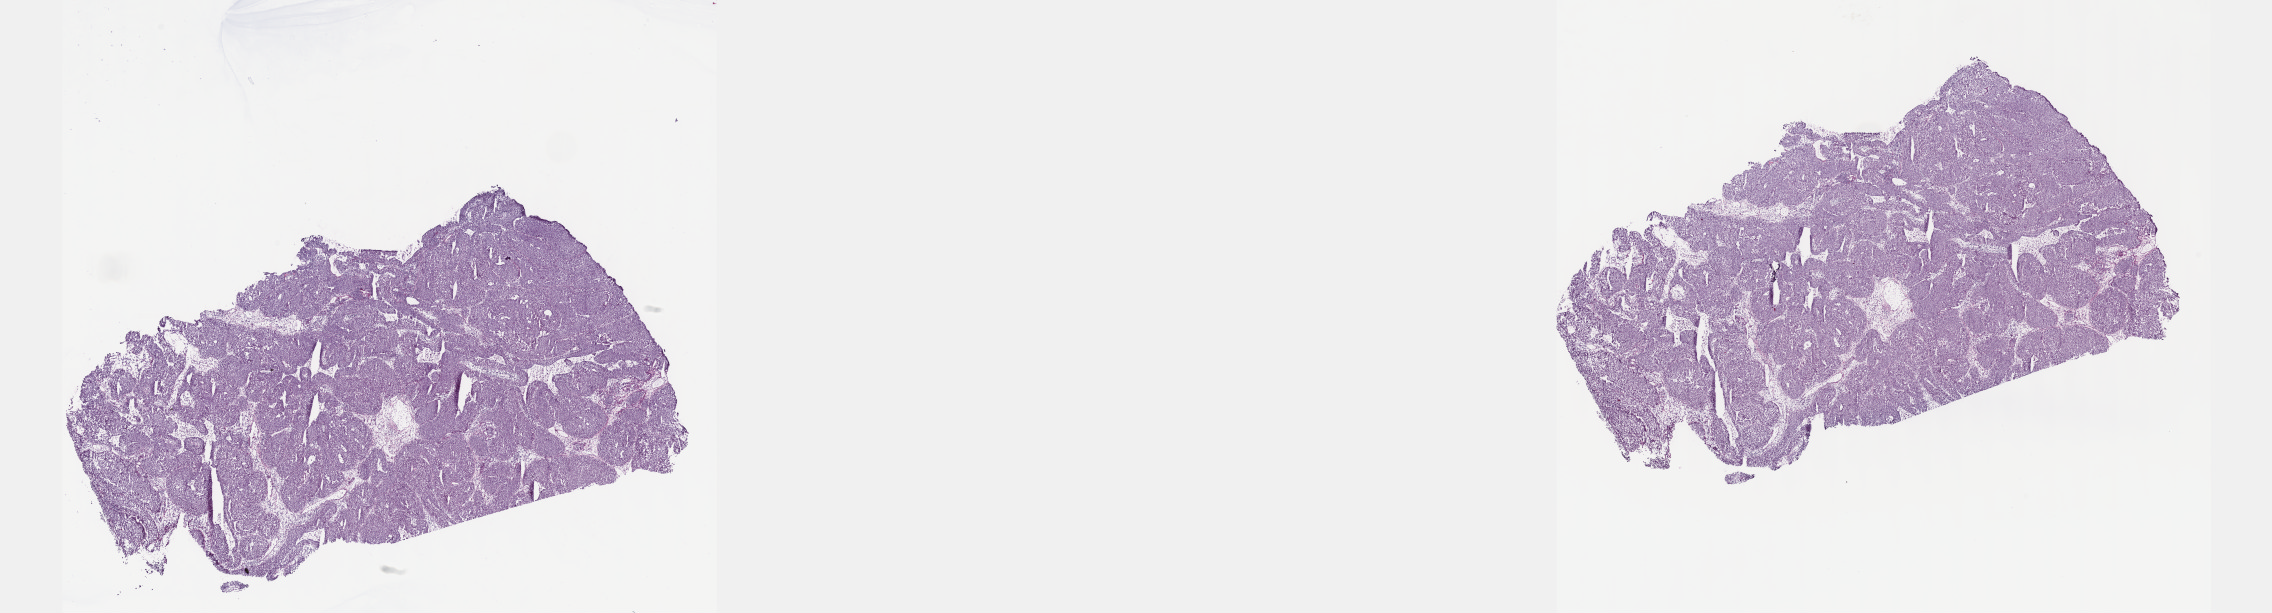
Digitized H&E tissue section (whole slide), shown as a low-resolution overview of the whole scanned area (about 36.7 x 9.9 mm, slide scanned at 40x); frozen section from the top of the tissue portion; primary tumour sample from the bladder. Patient: male, age at initial diagnosis 52 years. Histologic grade: low grade. Composition of this section per pathologist review: tumour cells 82%, tumour nuclei 90%, normal cells 0%, stromal cells 15%, necrosis 3%. Inflammatory infiltration, as recorded: lymphocyte infiltration 8%, monocyte infiltration 1%, neutrophil infiltration 3%.
Histologic diagnosis: Transitional cell carcinoma. TNM: T2 N0 M0. AJCC pathologic stage: II (7th edition).